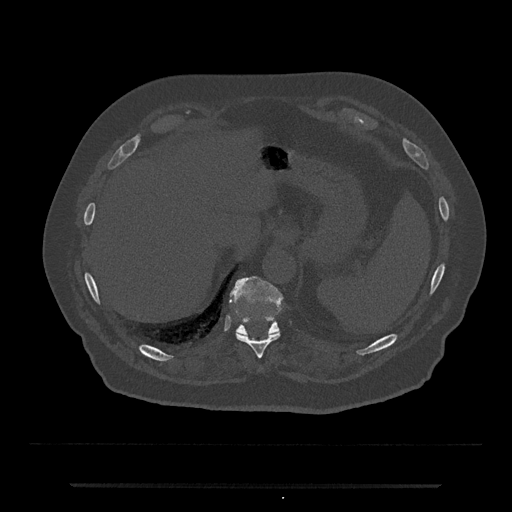
CT including the spine, one axial slice. Position 685 of 797 along the scan axis. 120 kVp. Bone window (W 1800 / L 400 HU). 0.5 mm slice thickness. 512 × 512 image matrix, field of view 434 × 434 mm. Patient: male, 80 years. From the clinical record (not read from this slice): primary cancer: prostate; vertebrae with lytic lesions (as recorded): L1, T11.
Annotated regions visible in this slice (semi-automatic segmentation, software-assisted and operator-edited):
- T10 vertebra: bounding box [x1, y1, x2, y2] px = [236, 331, 280, 359]
- T11 vertebra: [230, 276, 282, 335]